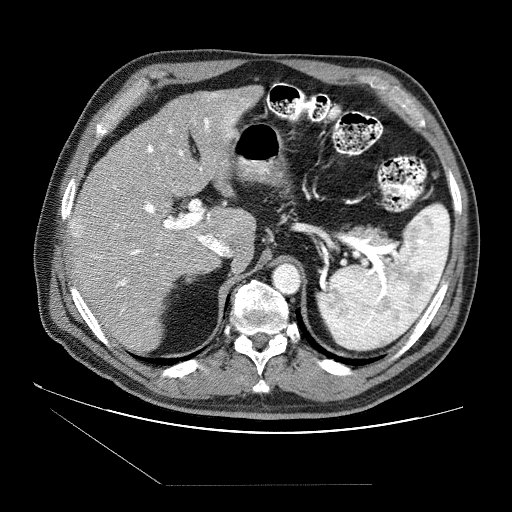
Contrast-enhanced abdominal CT (liver protocol), one axial slice. Slice 52 of 87 in the series (ordered by position). Soft-tissue window (W 400 / L 40 HU). 512 × 512 image matrix, field of view 400 × 400 mm. Case-level facts recorded for this patient, not image findings: diagnosis: hepatocellular carcinoma (patient treated with transarterial chemoembolisation; whether this scan precedes or follows treatment is not stated here); TNM stage (as recorded): Stage-II; Child-Pugh class: B; tumour size: 2.6 cm.
Outlined on this slice (semi-automatic segmentation, software-assisted and operator-edited):
- liver parenchyma outside the tumour (the mass and vessels are separate outlines, so this box may not span the whole liver): bounding box <70,86,262,350> (left, top, right, bottom; pixels)
- mass: <69,222,83,237>
- liver vessels: <73,93,249,310>